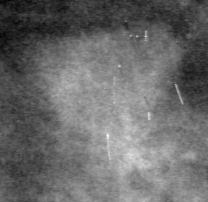
Region of interest cut from a scanned film mammogram (one marked finding), right breast, MLO view, BI-RADS breast density category 2 (scale 1–4).
Finding: mass, shape lobulated, margins obscured; BI-RADS assessment category 4; pathology result (as recorded, not read from the image): malignant.